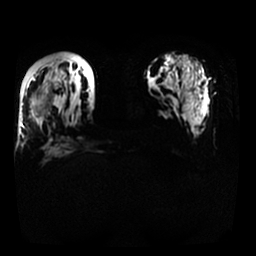
Breast MRI, one axial slice. Slice 10 of 25 in the series (ordered by position). Diffusion-weighted series; image 2 of 4 stored at this slice position (different b-values; order by instance number). 1.5 T. 4 mm slice thickness. 256 × 256 image matrix. Female patient.
Outlined on this slice (manually delineated by an expert):
- tumour on diffusion-weighted imaging: bounding box (x1, y1, x2, y2) in pixels: (32, 95, 45, 115)